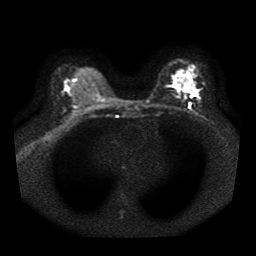
Breast MRI, one axial slice; position 27 of 41 along the scan axis; diffusion-weighted series; image 2 of 4 stored at this slice position (different b-values; order by instance number); 1.5 T; 5 mm slice thickness; 256 × 256 image matrix, field of view 330 × 330 mm. Female patient.
Structures marked on this image (expert manual segmentation):
- tumour on diffusion-weighted imaging: bounding box <184,86,193,94> (left, top, right, bottom; pixels)